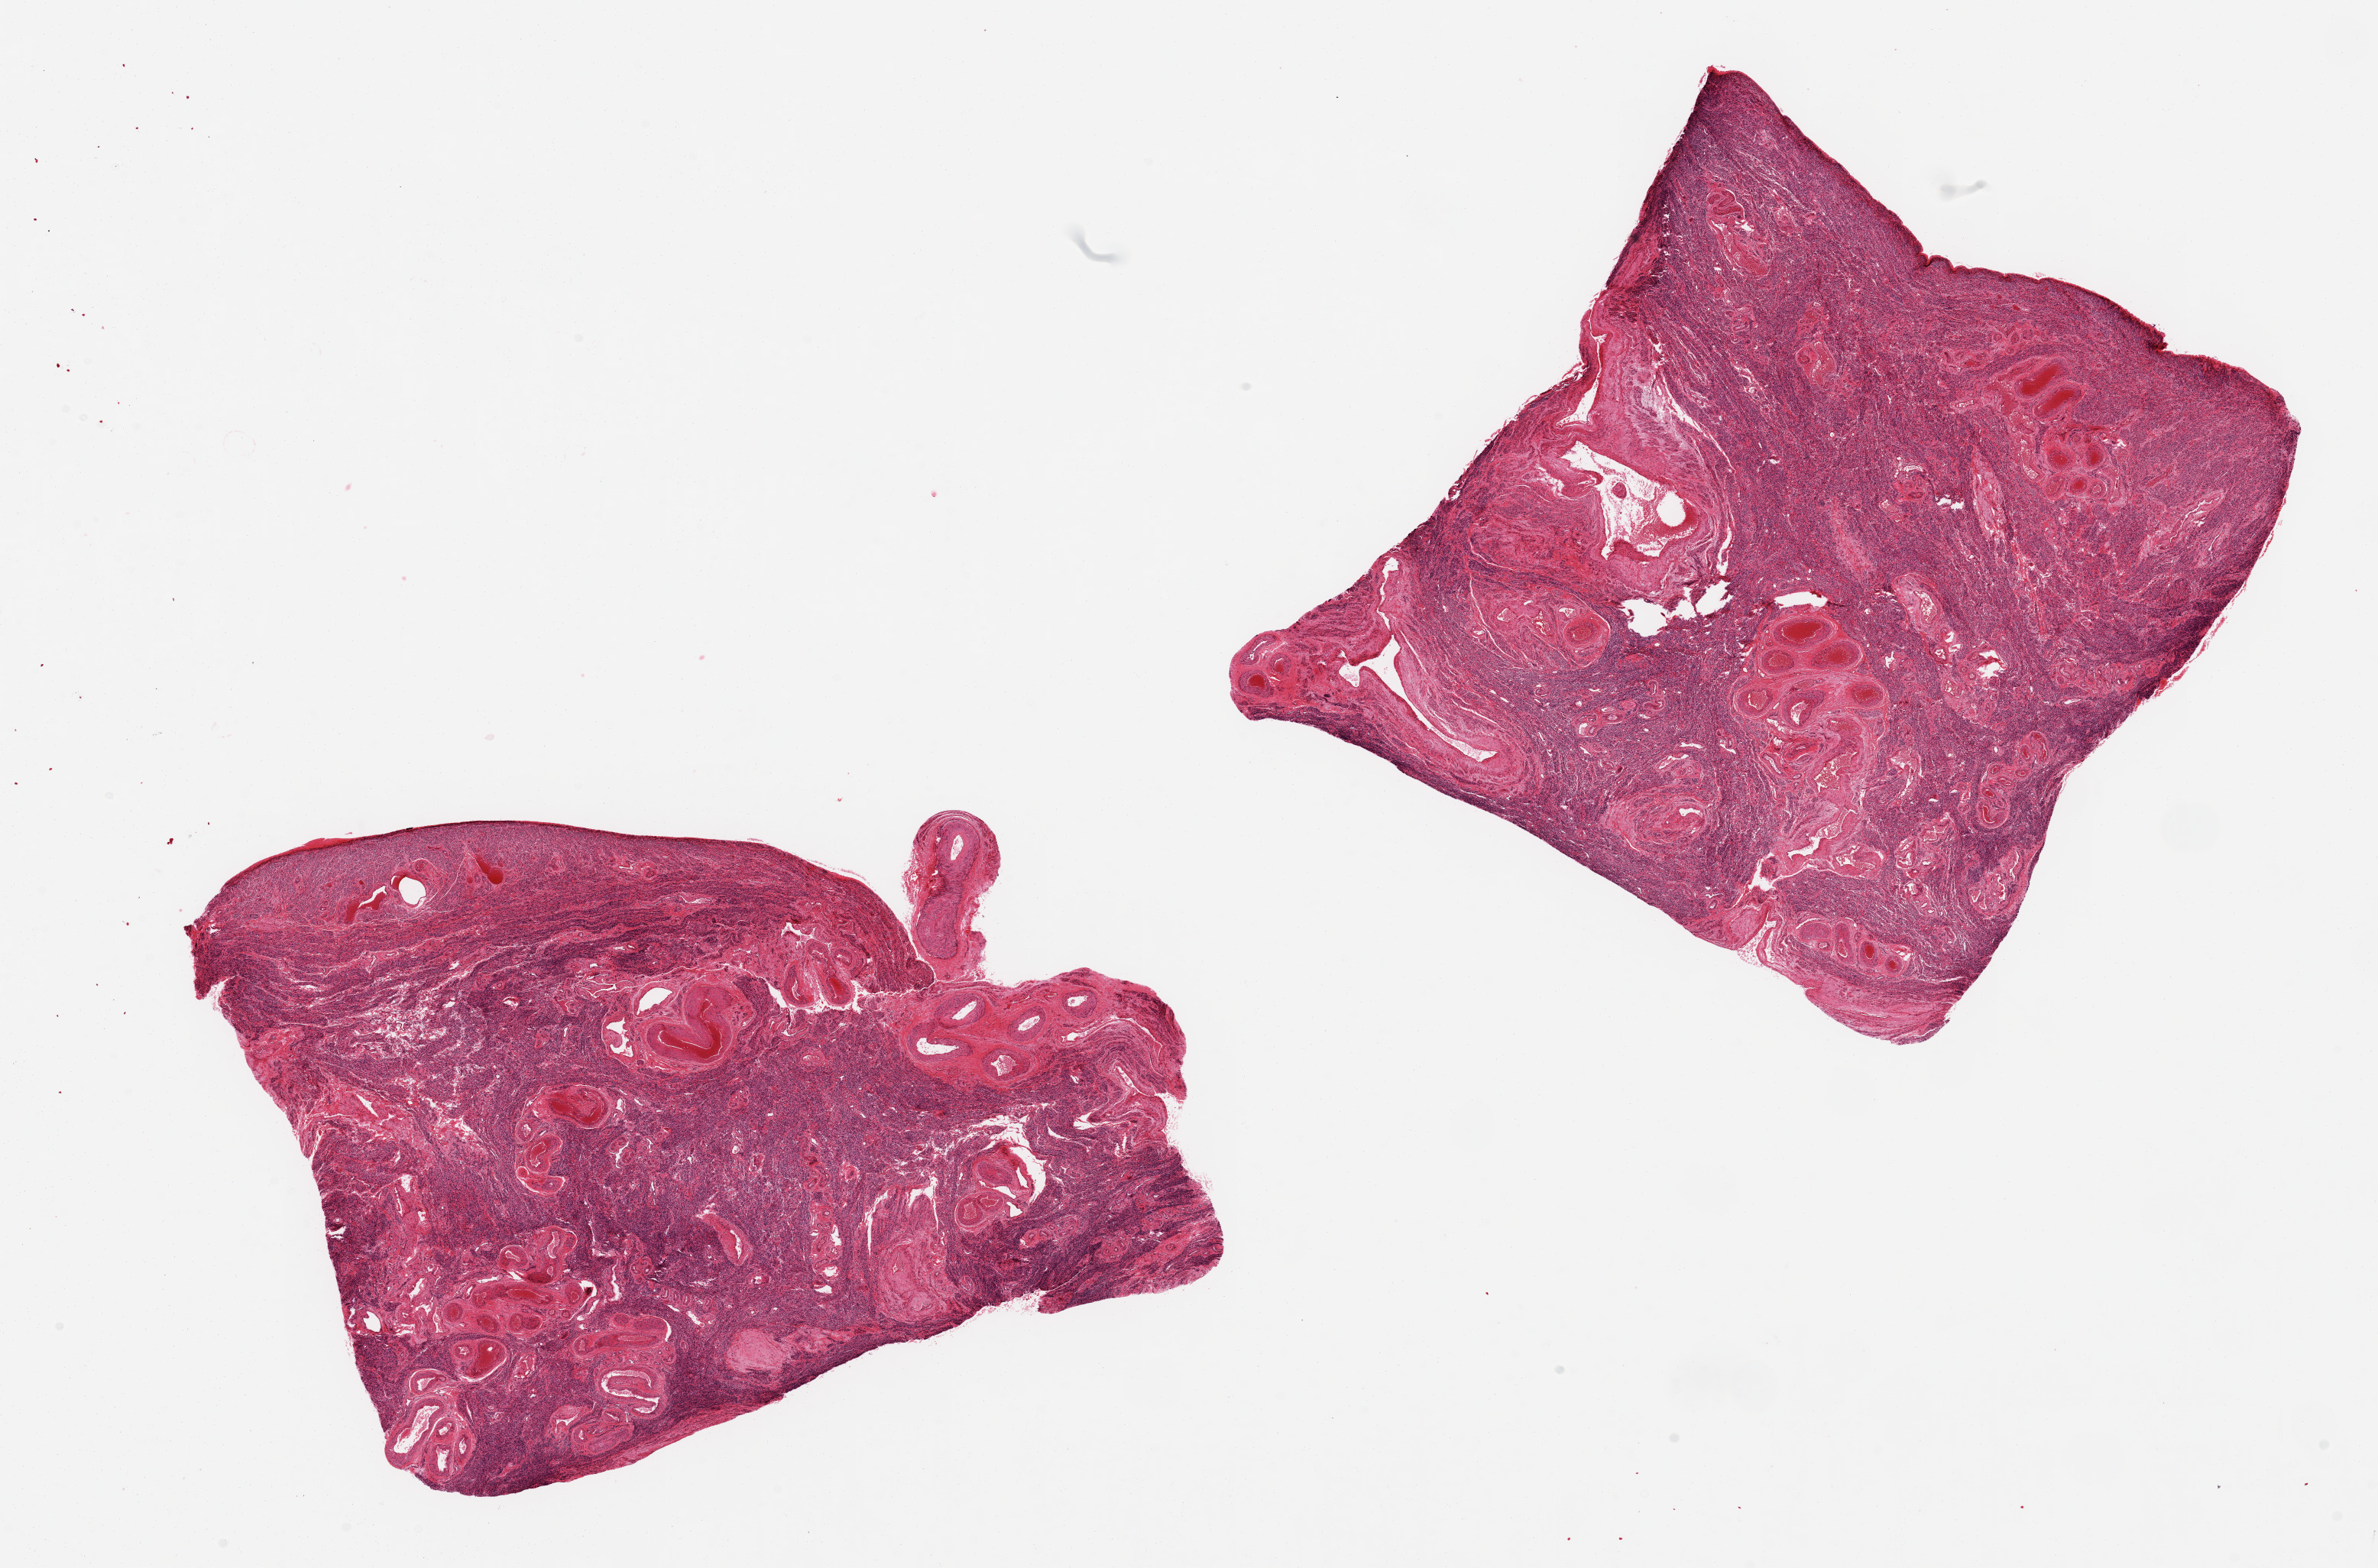
Digitized H&E-stained section, brightfield — whole scanned area (about 24.6 x 16.2 mm) shown as a low-resolution overview, PAXgene-fixed, paraffin-embedded tissue, sampled site (target tissue): uterus, tissue donor sample. Donor: female.
• review note (as recorded): 2 pieces, 9x7 & 7x7s; no glands